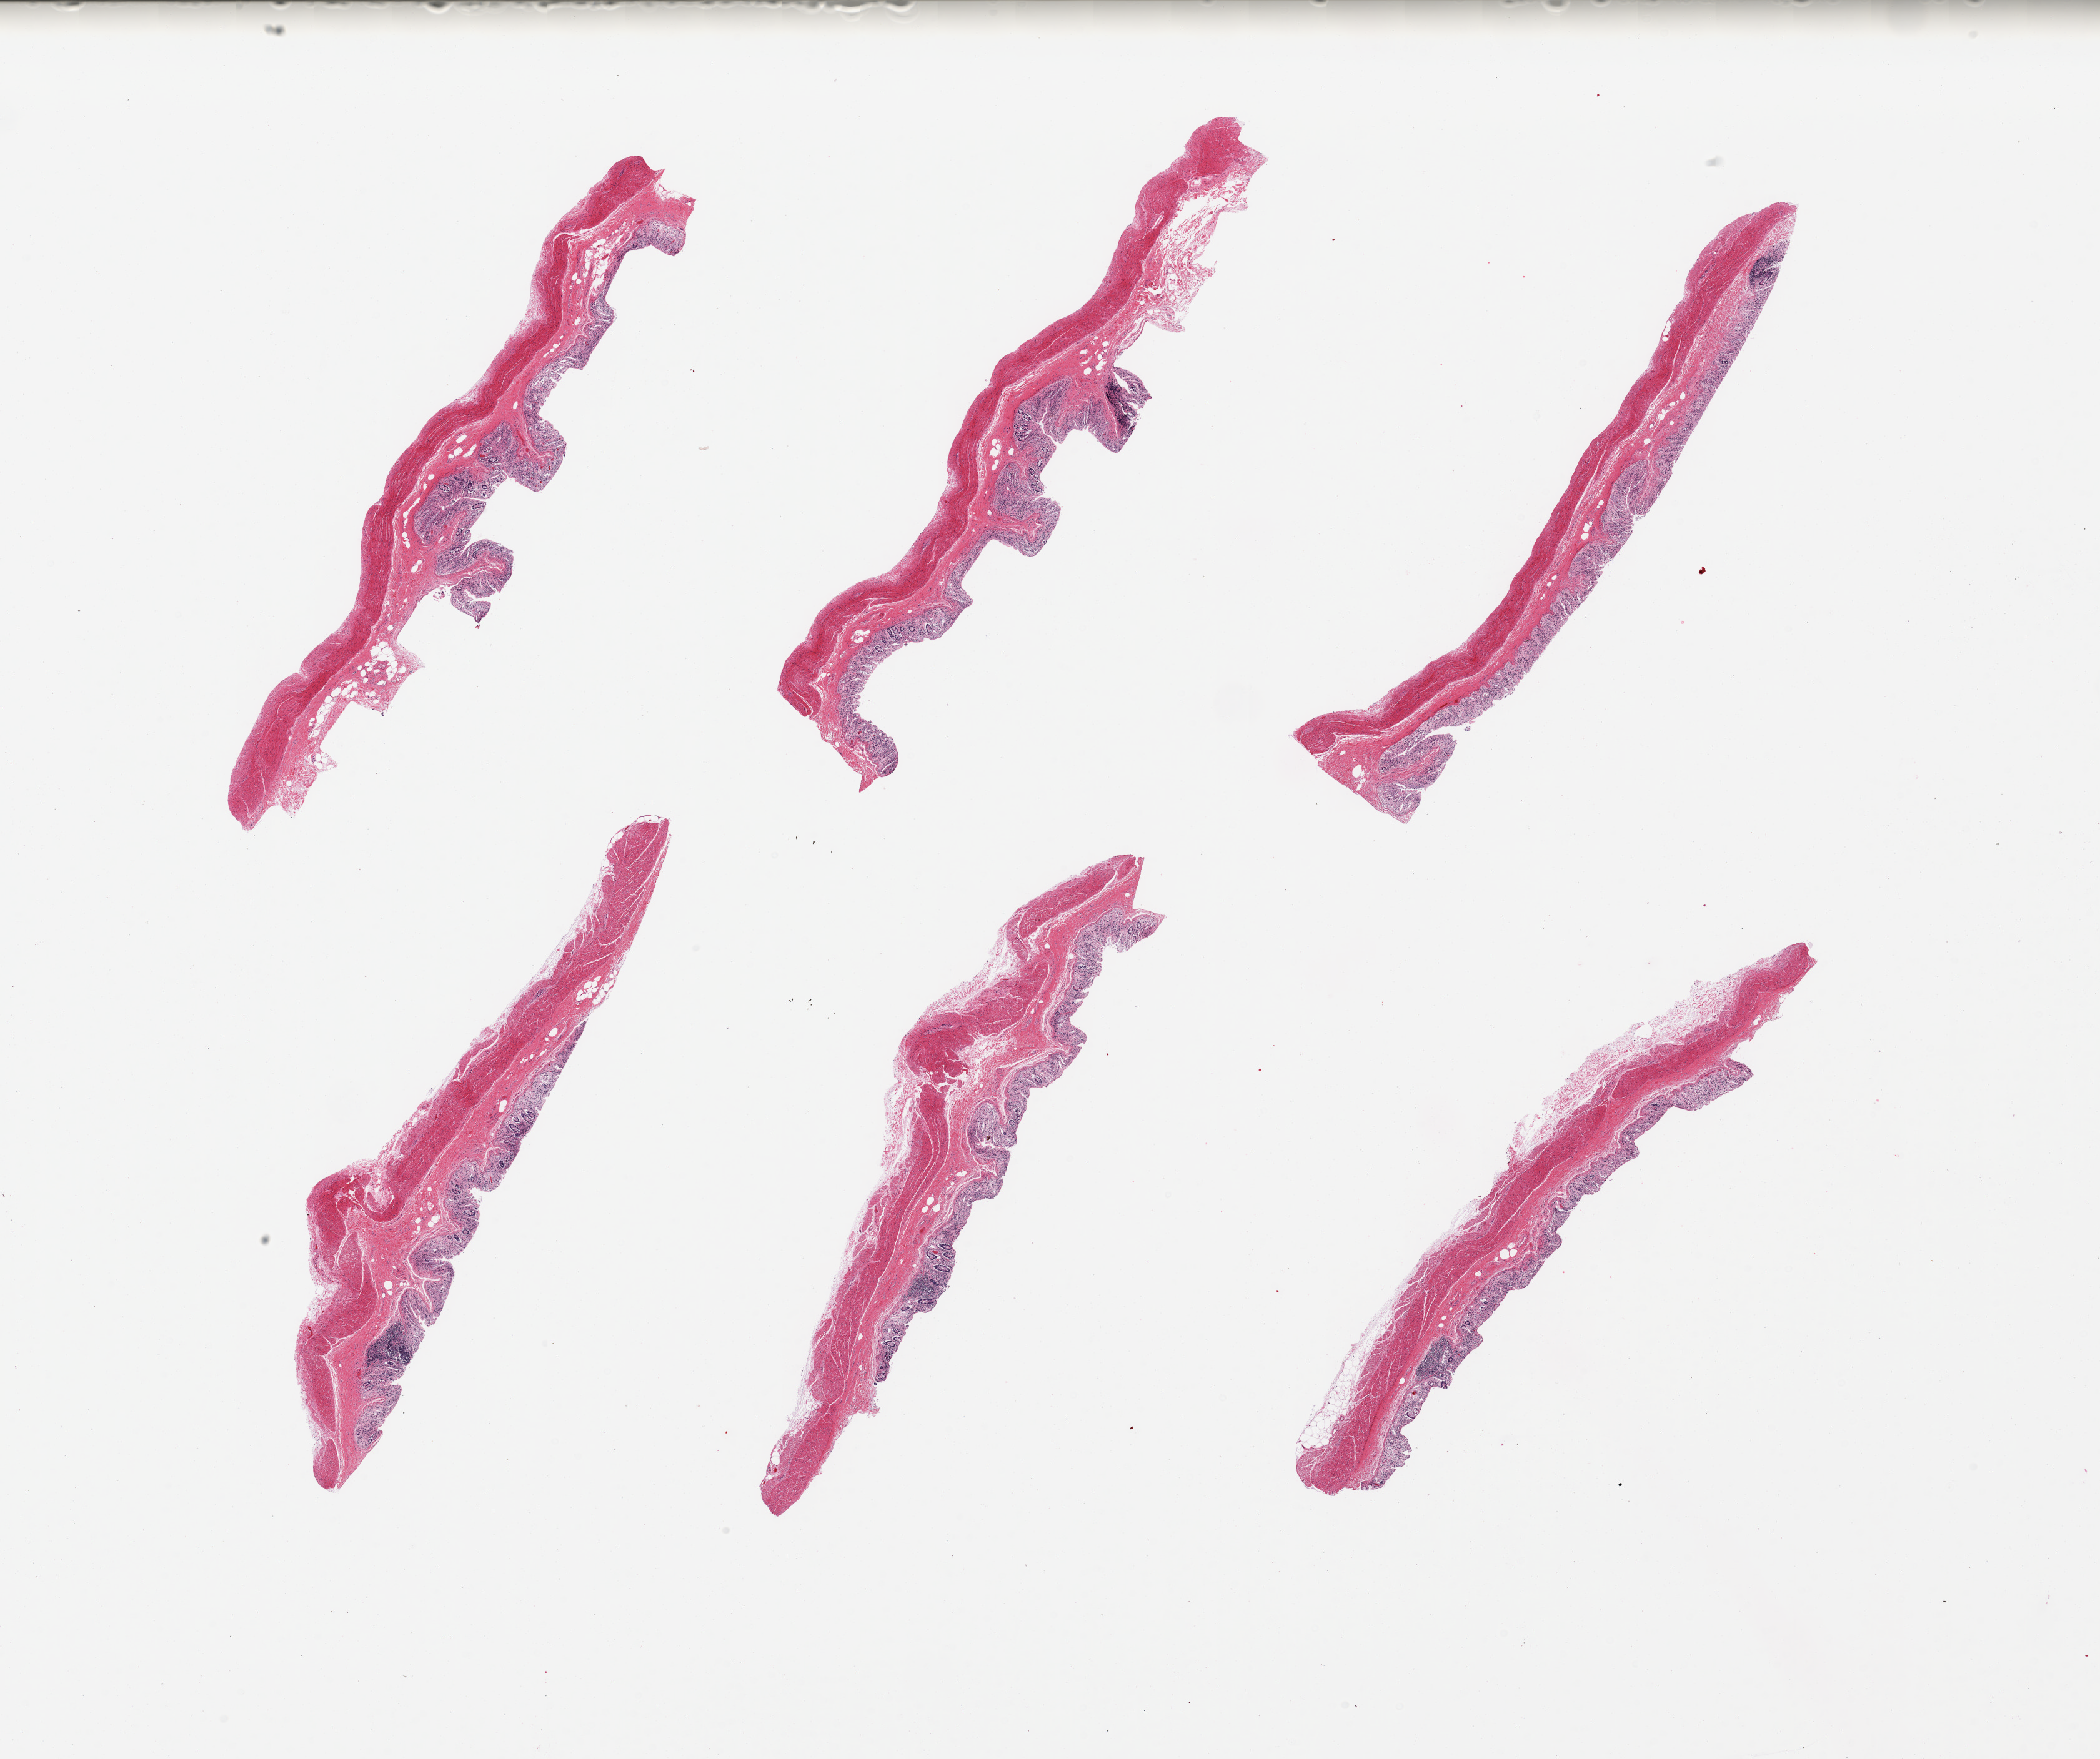
Haematoxylin and eosin whole-slide image — low-resolution overview of the scanned area, about 26.6 x 22.3 mm. PAXgene-fixed paraffin-embedded (PFPE) section. Target tissue: transverse colon. Donor tissue sample.
* pathologist's review note for this sample: 6 pieces; moderate to severe mucosal autolysis and preserved muscularis